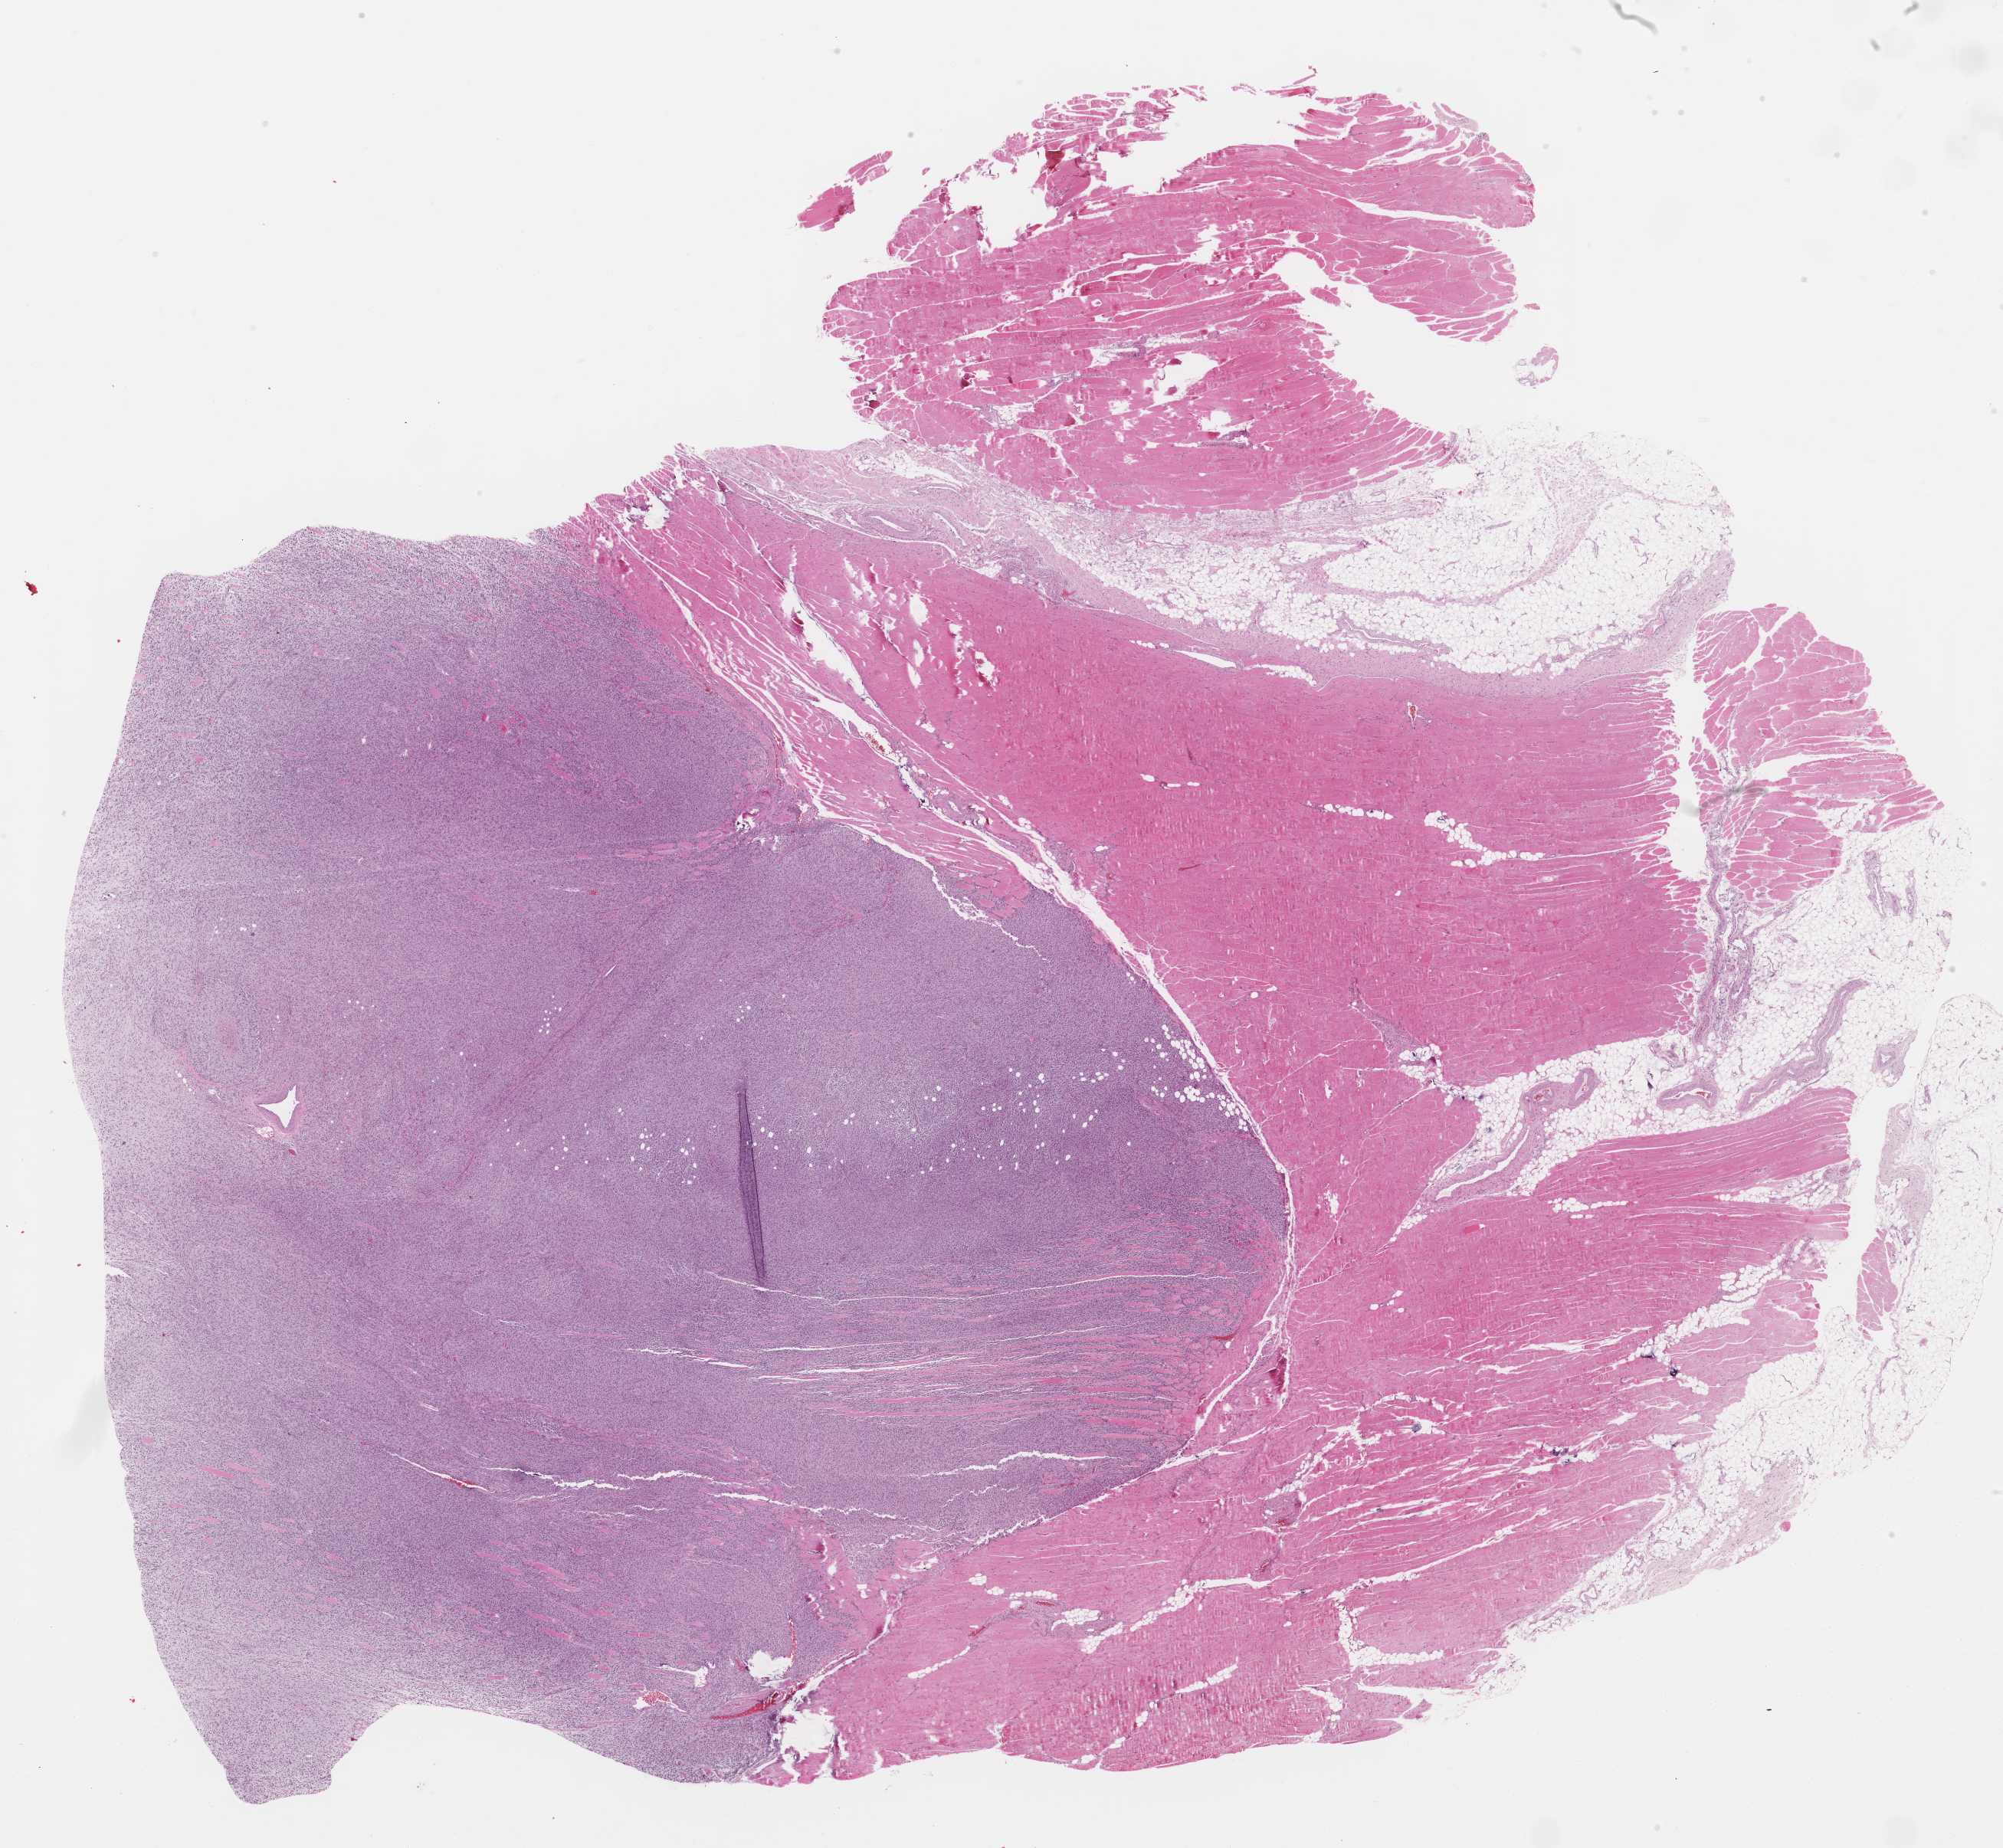
Whole-slide histology image, H&E, low-resolution overview of the scanned area, about 21.1 x 19.5 mm (slide scanned at 40x); formalin-fixed paraffin-embedded (FFPE) diagnostic section; connective, subcutaneous and other soft tissues, primary tumour sample. Female patient; age at initial diagnosis 86 years.
• histologic diagnosis: Fibromyxosarcoma (connective, subcutaneous and other soft tissues of pelvis)